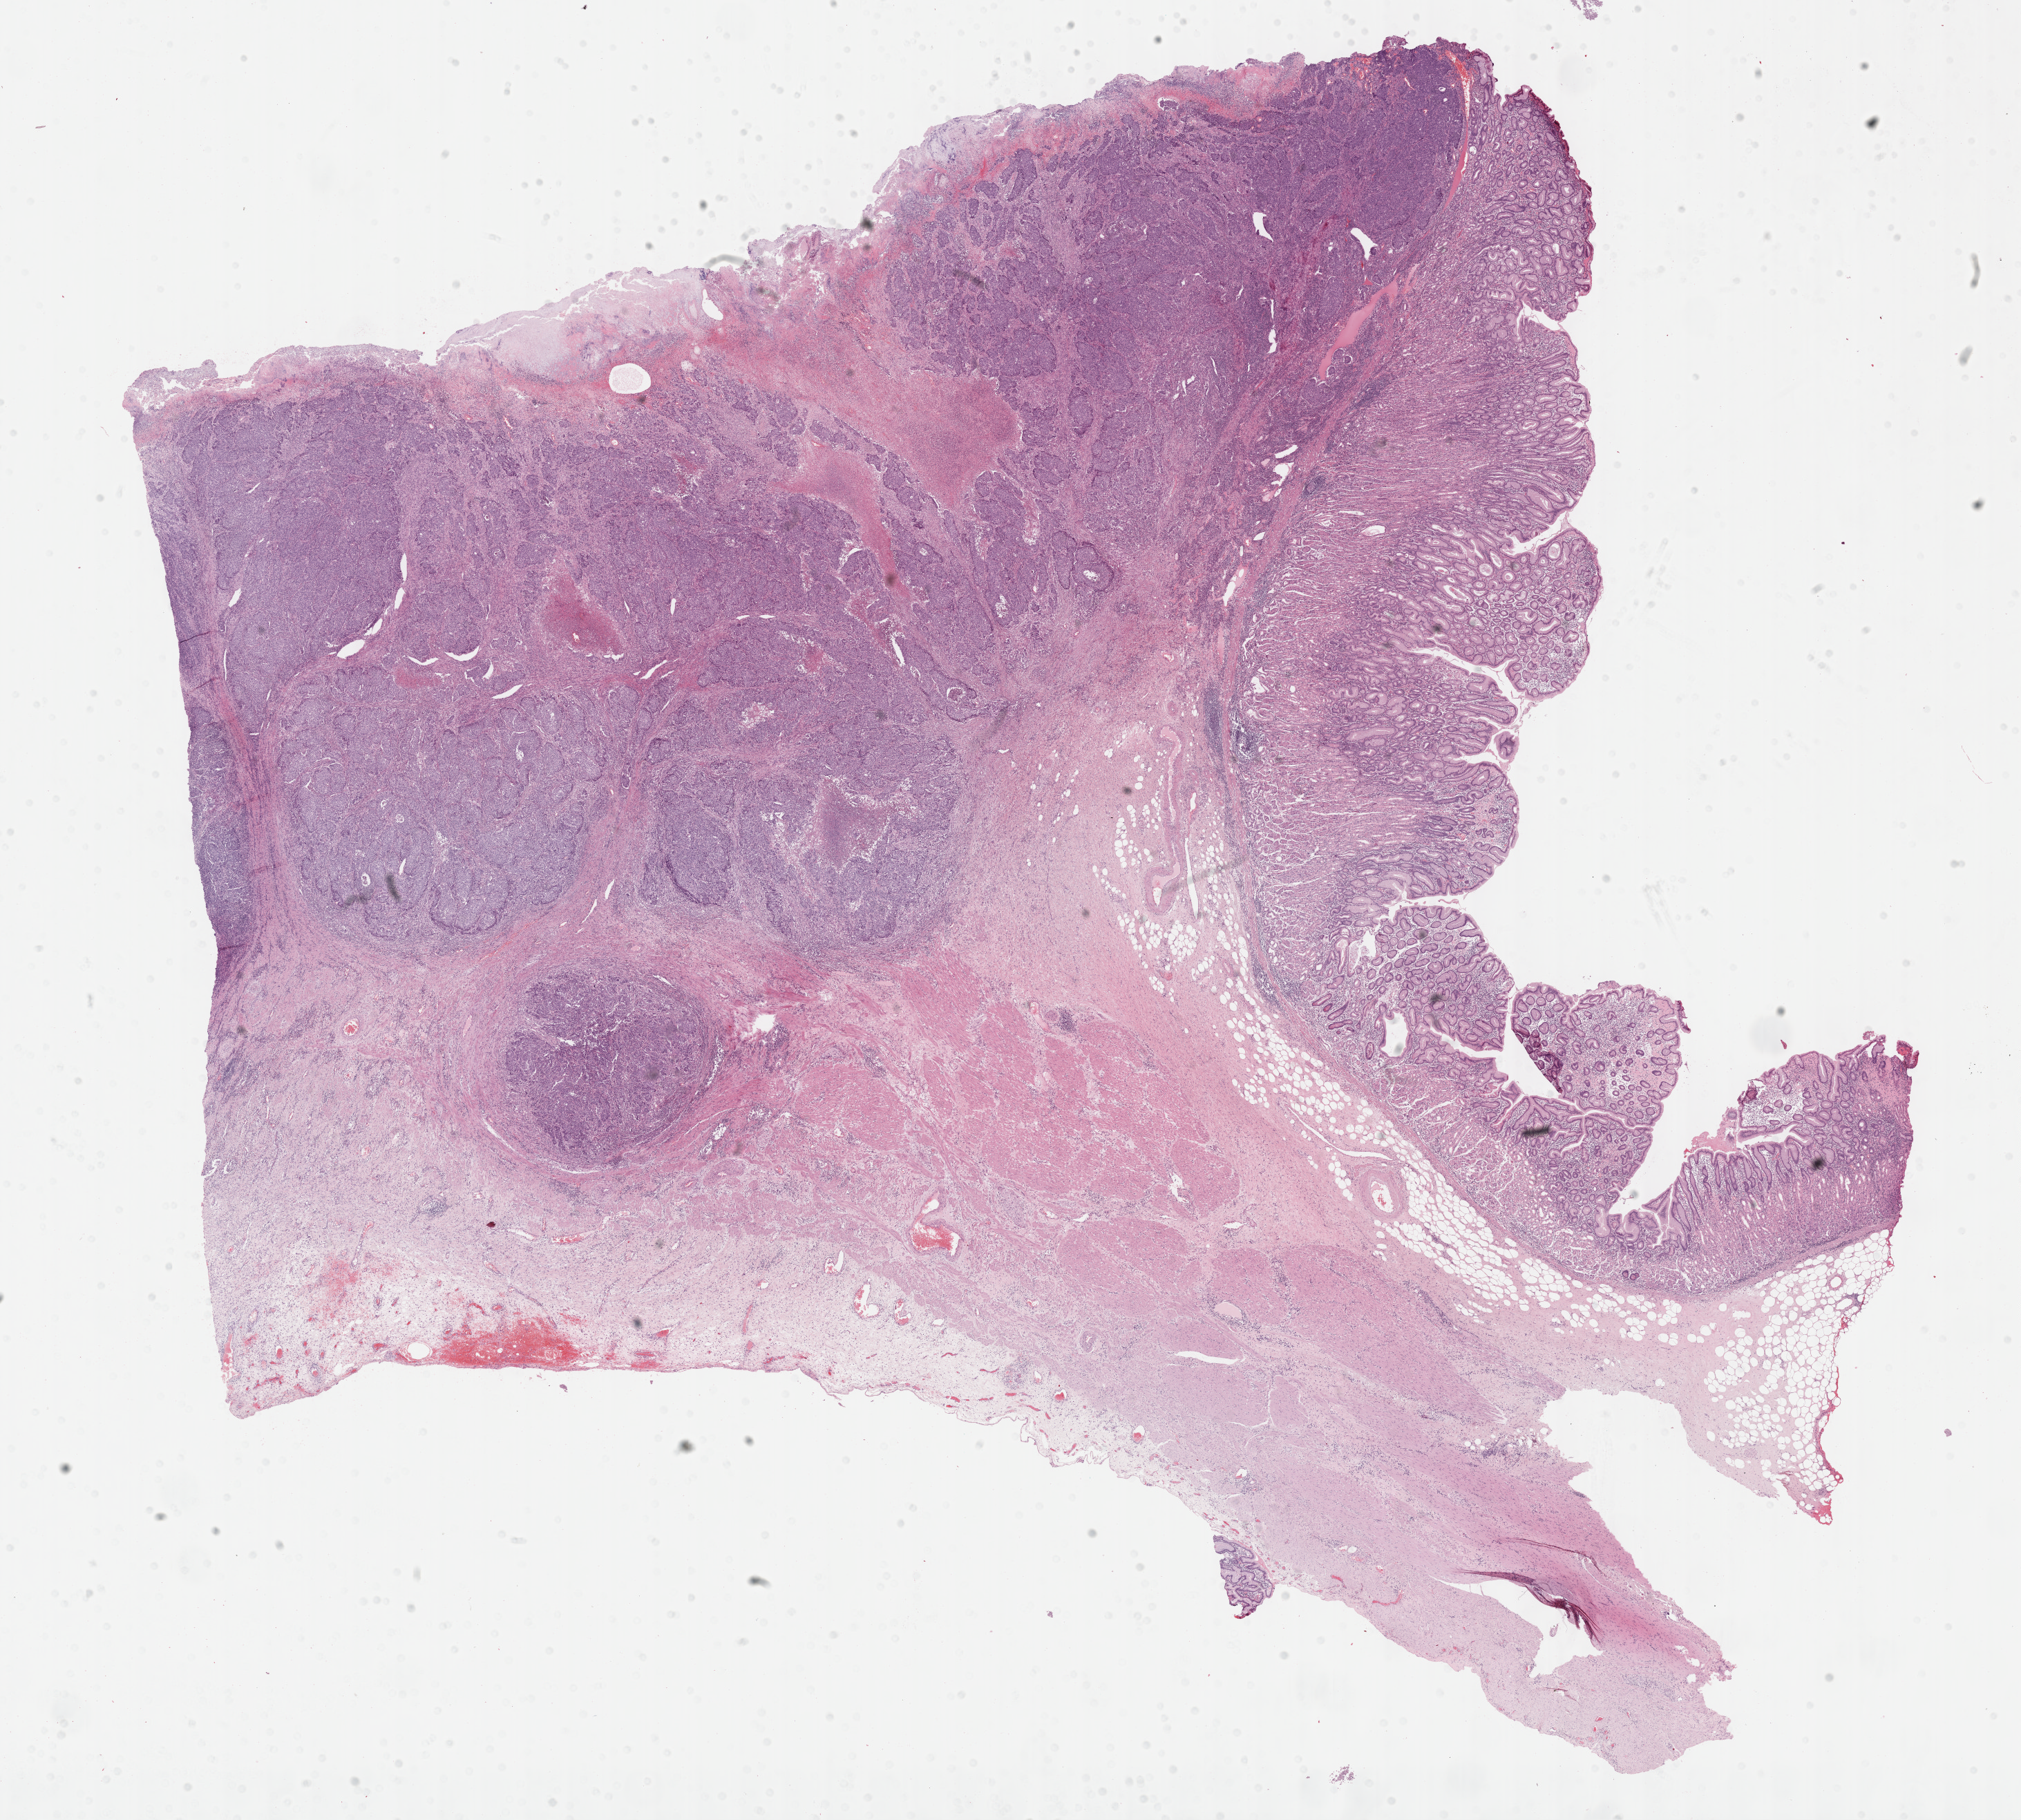
Whole-slide histology image, H&E-stained, low-resolution overview of the scanned area, about 23.7 x 21.3 mm (acquisition: 40x scan). Formalin-fixed paraffin-embedded (FFPE) diagnostic section. Stomach, primary tumour sample. Patient: male, age at initial diagnosis 66 years. Histologic grade: G3 (poorly differentiated).
* AJCC pathologic stage: IIIA
* pathologic diagnosis: Adenocarcinoma, intestinal type (fundus of stomach)